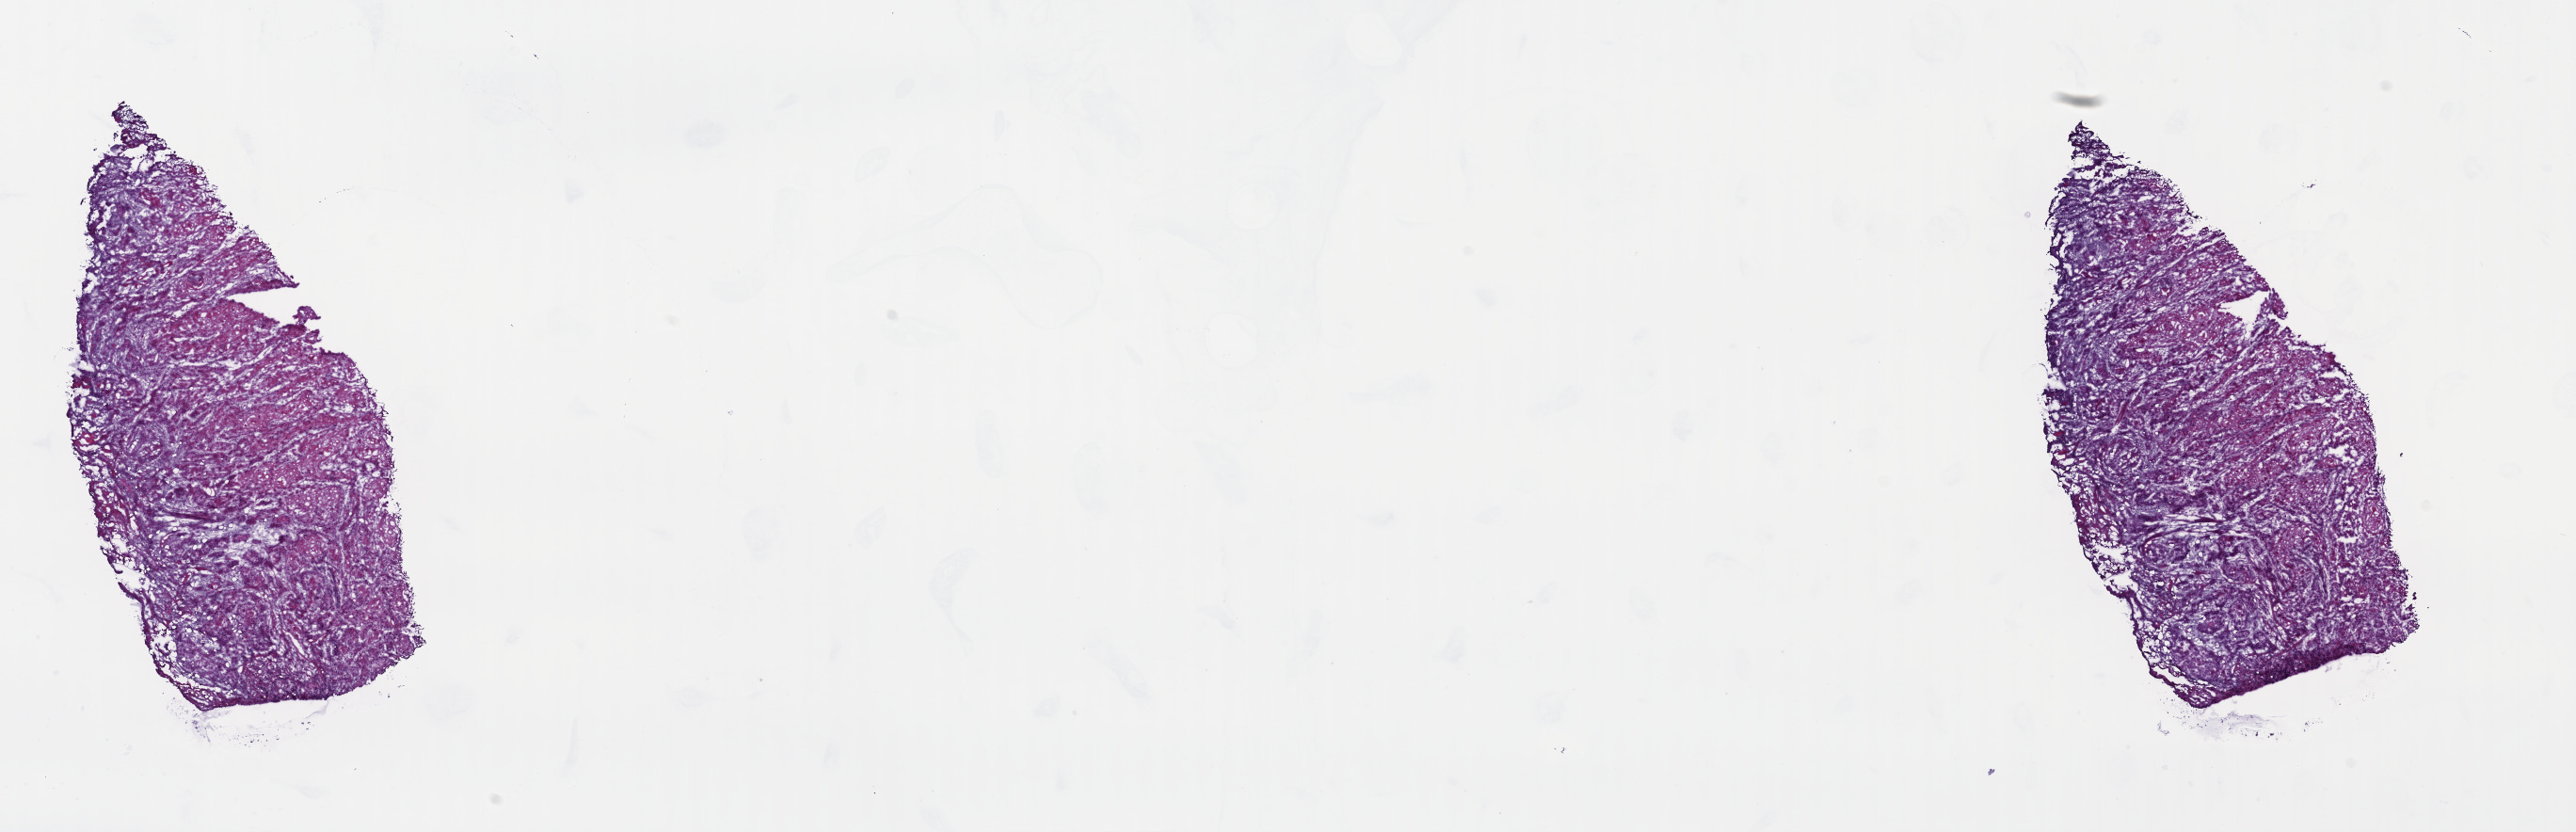
Digitized Hematoxylin and eosin (H&E) stained tissue section (whole slide), whole scanned area (about 21.5 x 6.9 mm) shown as a low-resolution overview; frozen section; sample: primary tumour, head and neck. Male patient; age at initial diagnosis 53 years. Histologic grade: G1 (well differentiated). Pathologist review of this section (percent, as recorded): tumour cells 80%, tumour nuclei 80%, normal cells 0%, stromal cells 10%, necrosis 10%. Inflammatory infiltration, as recorded: lymphocyte infiltration 40%, monocyte infiltration 20%, neutrophil infiltration 20%.
- pathologic diagnosis: Squamous cell carcinoma, NOS (mouth, NOS)